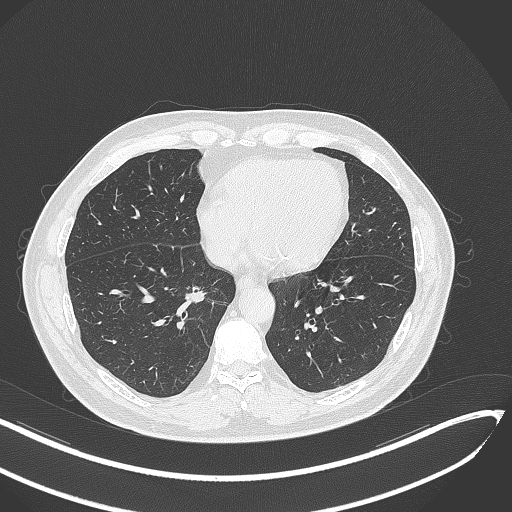
Chest CT, one axial slice; position 135 of 429 along the scan axis; reconstruction kernel B70f; lung window (W 1500 / L -600 HU); 1 mm slice thickness; 512 × 512 image matrix, field of view 400 × 400 mm. Patient: male, 62 years. Case-level facts recorded for this patient, not image findings: clinical TNM (as recorded): T1b N0 M0; histopathological grade: G2.
Annotated regions visible in this slice (rectangle marked by the reading radiologist):
- lung tumour (recorded histology: adenocarcinoma): bounding box [x1, y1, x2, y2] px = [183, 285, 213, 309]